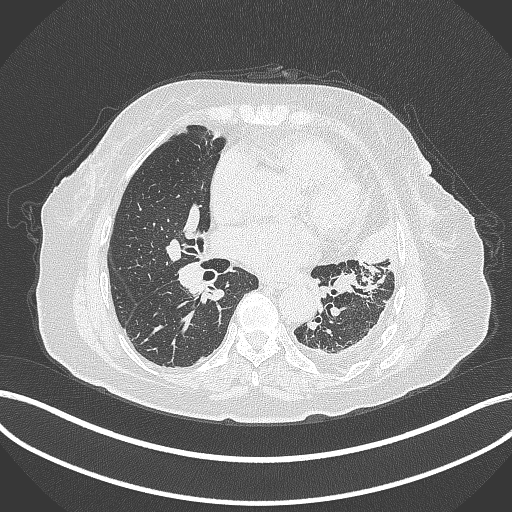
Chest CT, one axial slice. Slice 174 of 399 in the series (ordered by position). 120 kVp. Lung window (W 1500 / L -600 HU). 1 mm slice thickness. 512 × 512 image matrix, field of view 400 × 400 mm. Female patient, age 75 years. From the clinical record (not read from this slice): clinical TNM (as recorded): T3 N3 M1.
Outlined on this slice (rectangle marked by the reading radiologist):
- lung tumour (recorded histology: adenocarcinoma): bounding box [x1, y1, x2, y2] px = [352, 222, 401, 273]